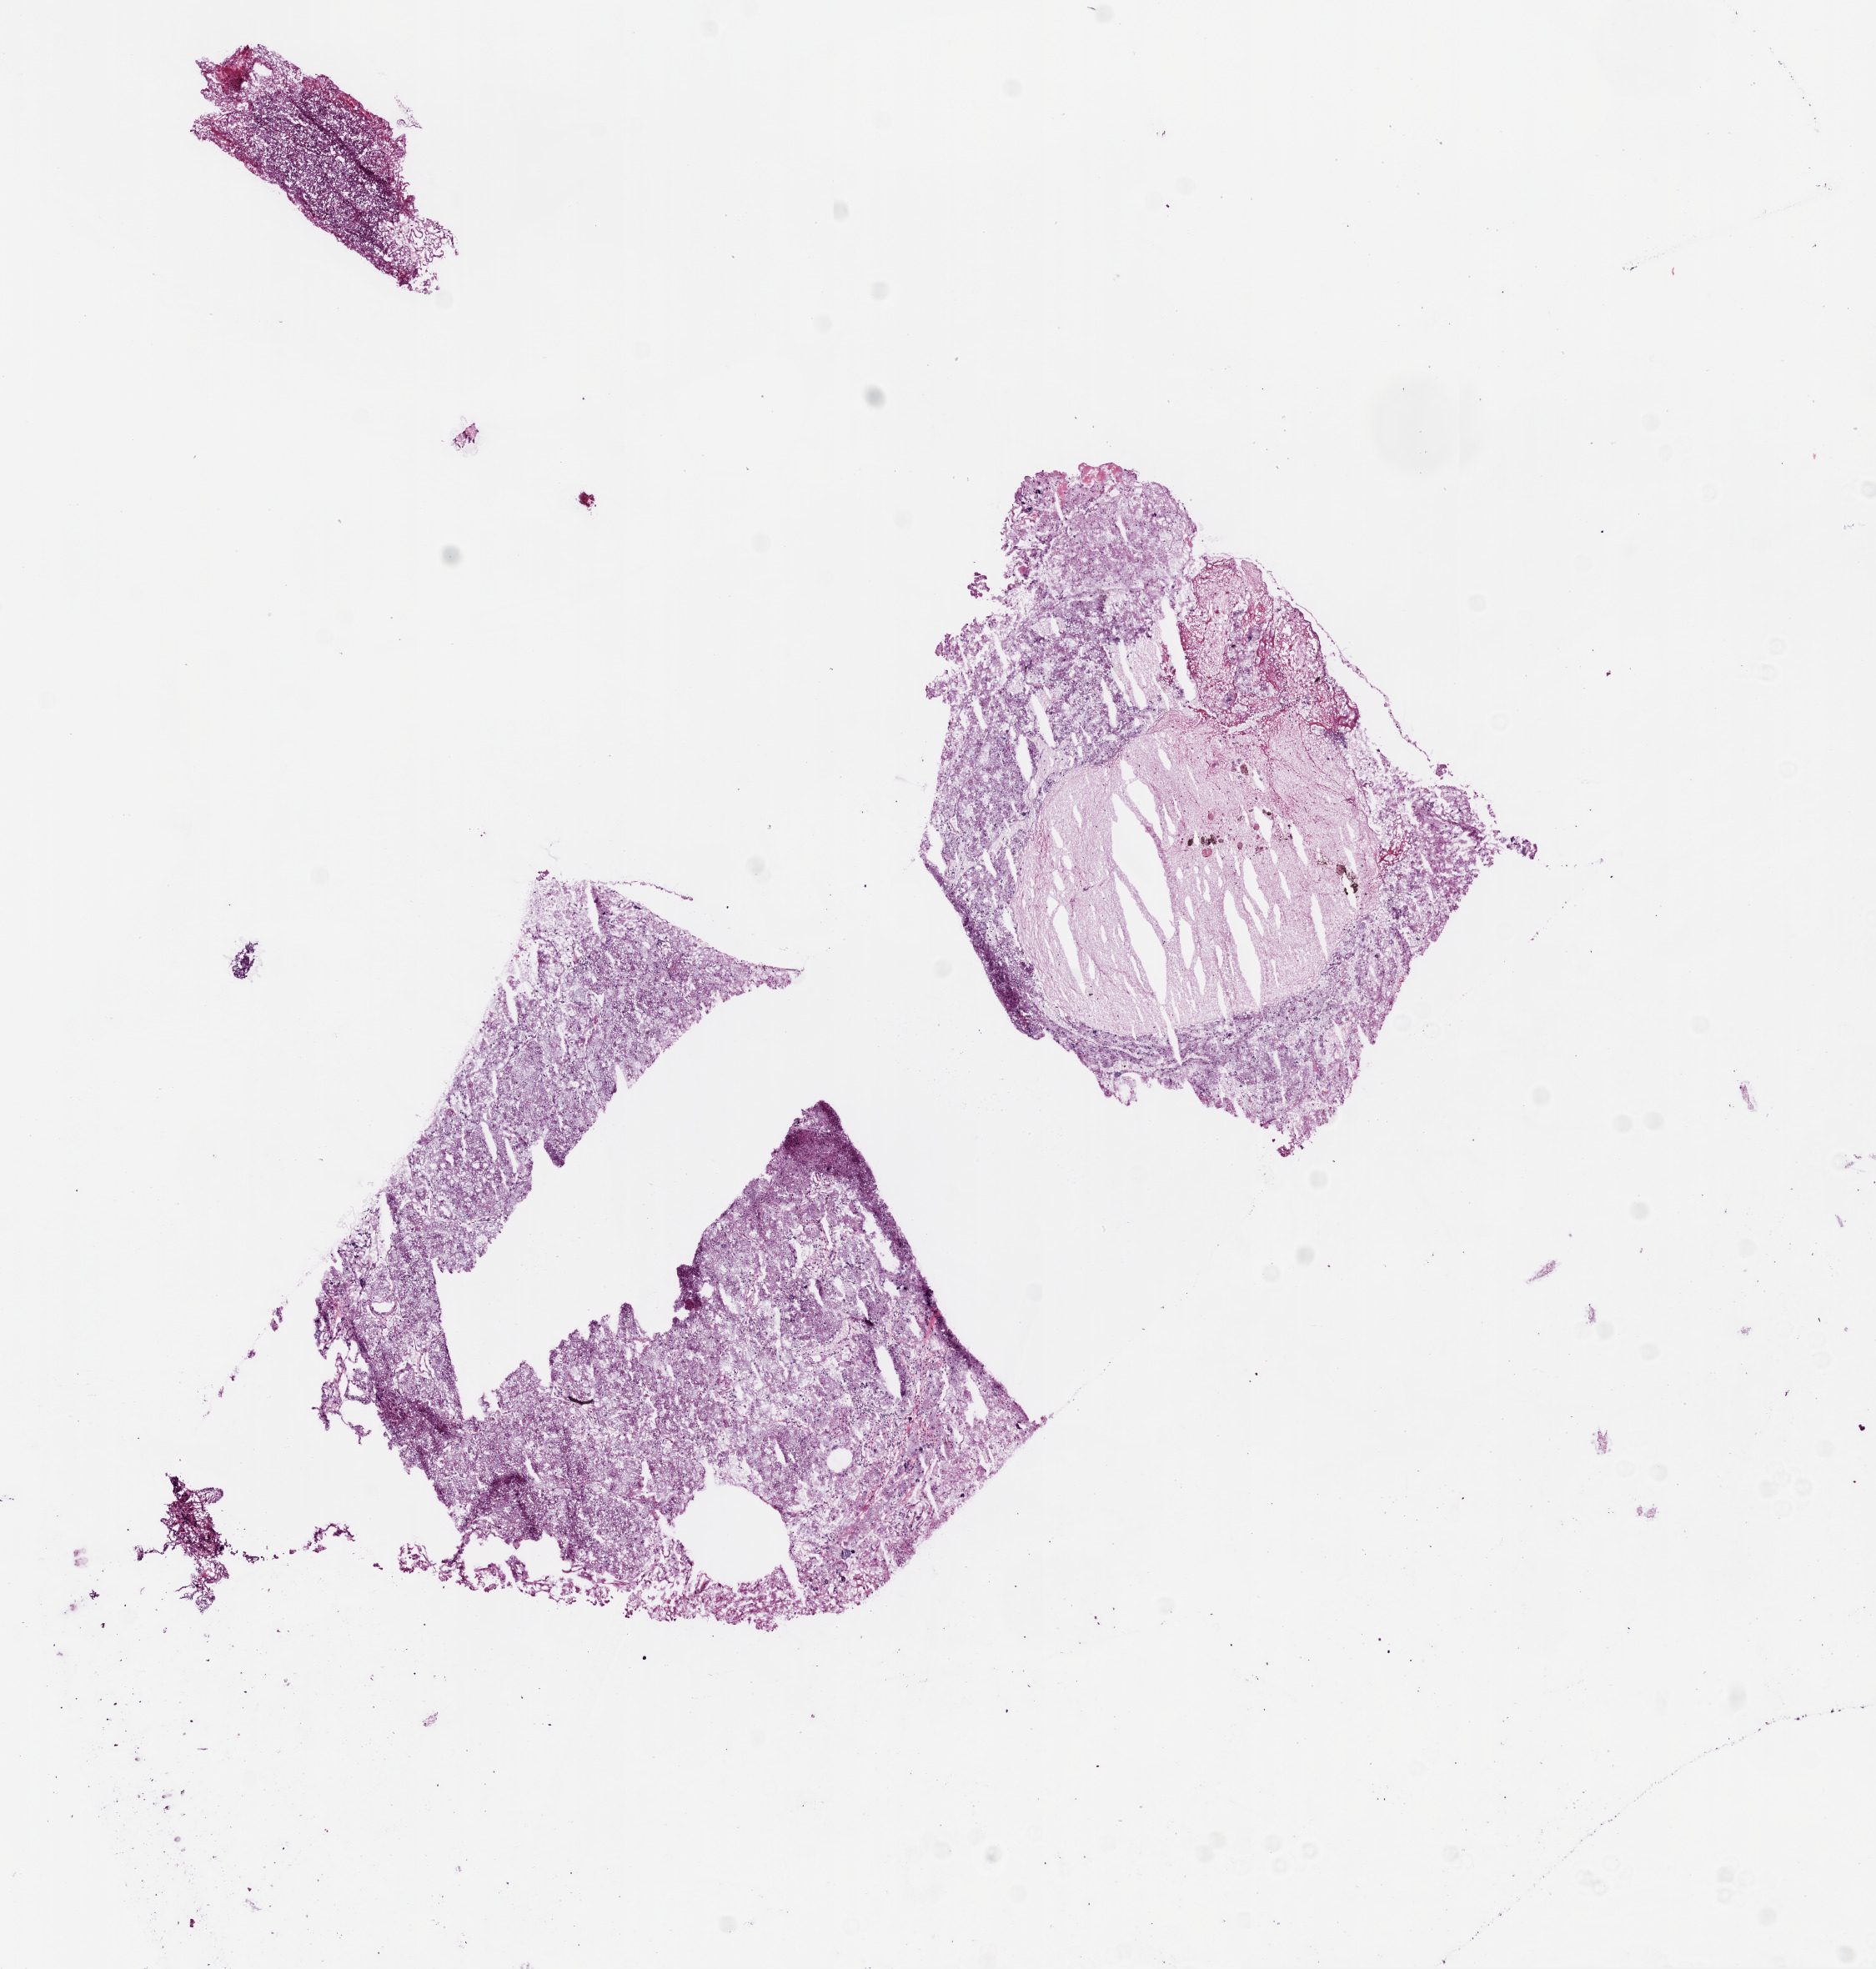
Digitized H&E-stained tissue section (whole slide), low-resolution overview of the scanned area, about 9.0 x 9.5 mm; frozen section from the bottom of the tissue portion; sample: primary tumour, kidney. Patient: male, age at initial diagnosis 63 years. Composition of this section per pathologist review: tumour cells 90%, tumour nuclei 70%, normal cells 0%, stromal cells 10%, necrosis 0%.
Diagnosis: Clear cell adenocarcinoma, NOS. AJCC pathologic stage: I. Laterality: left.